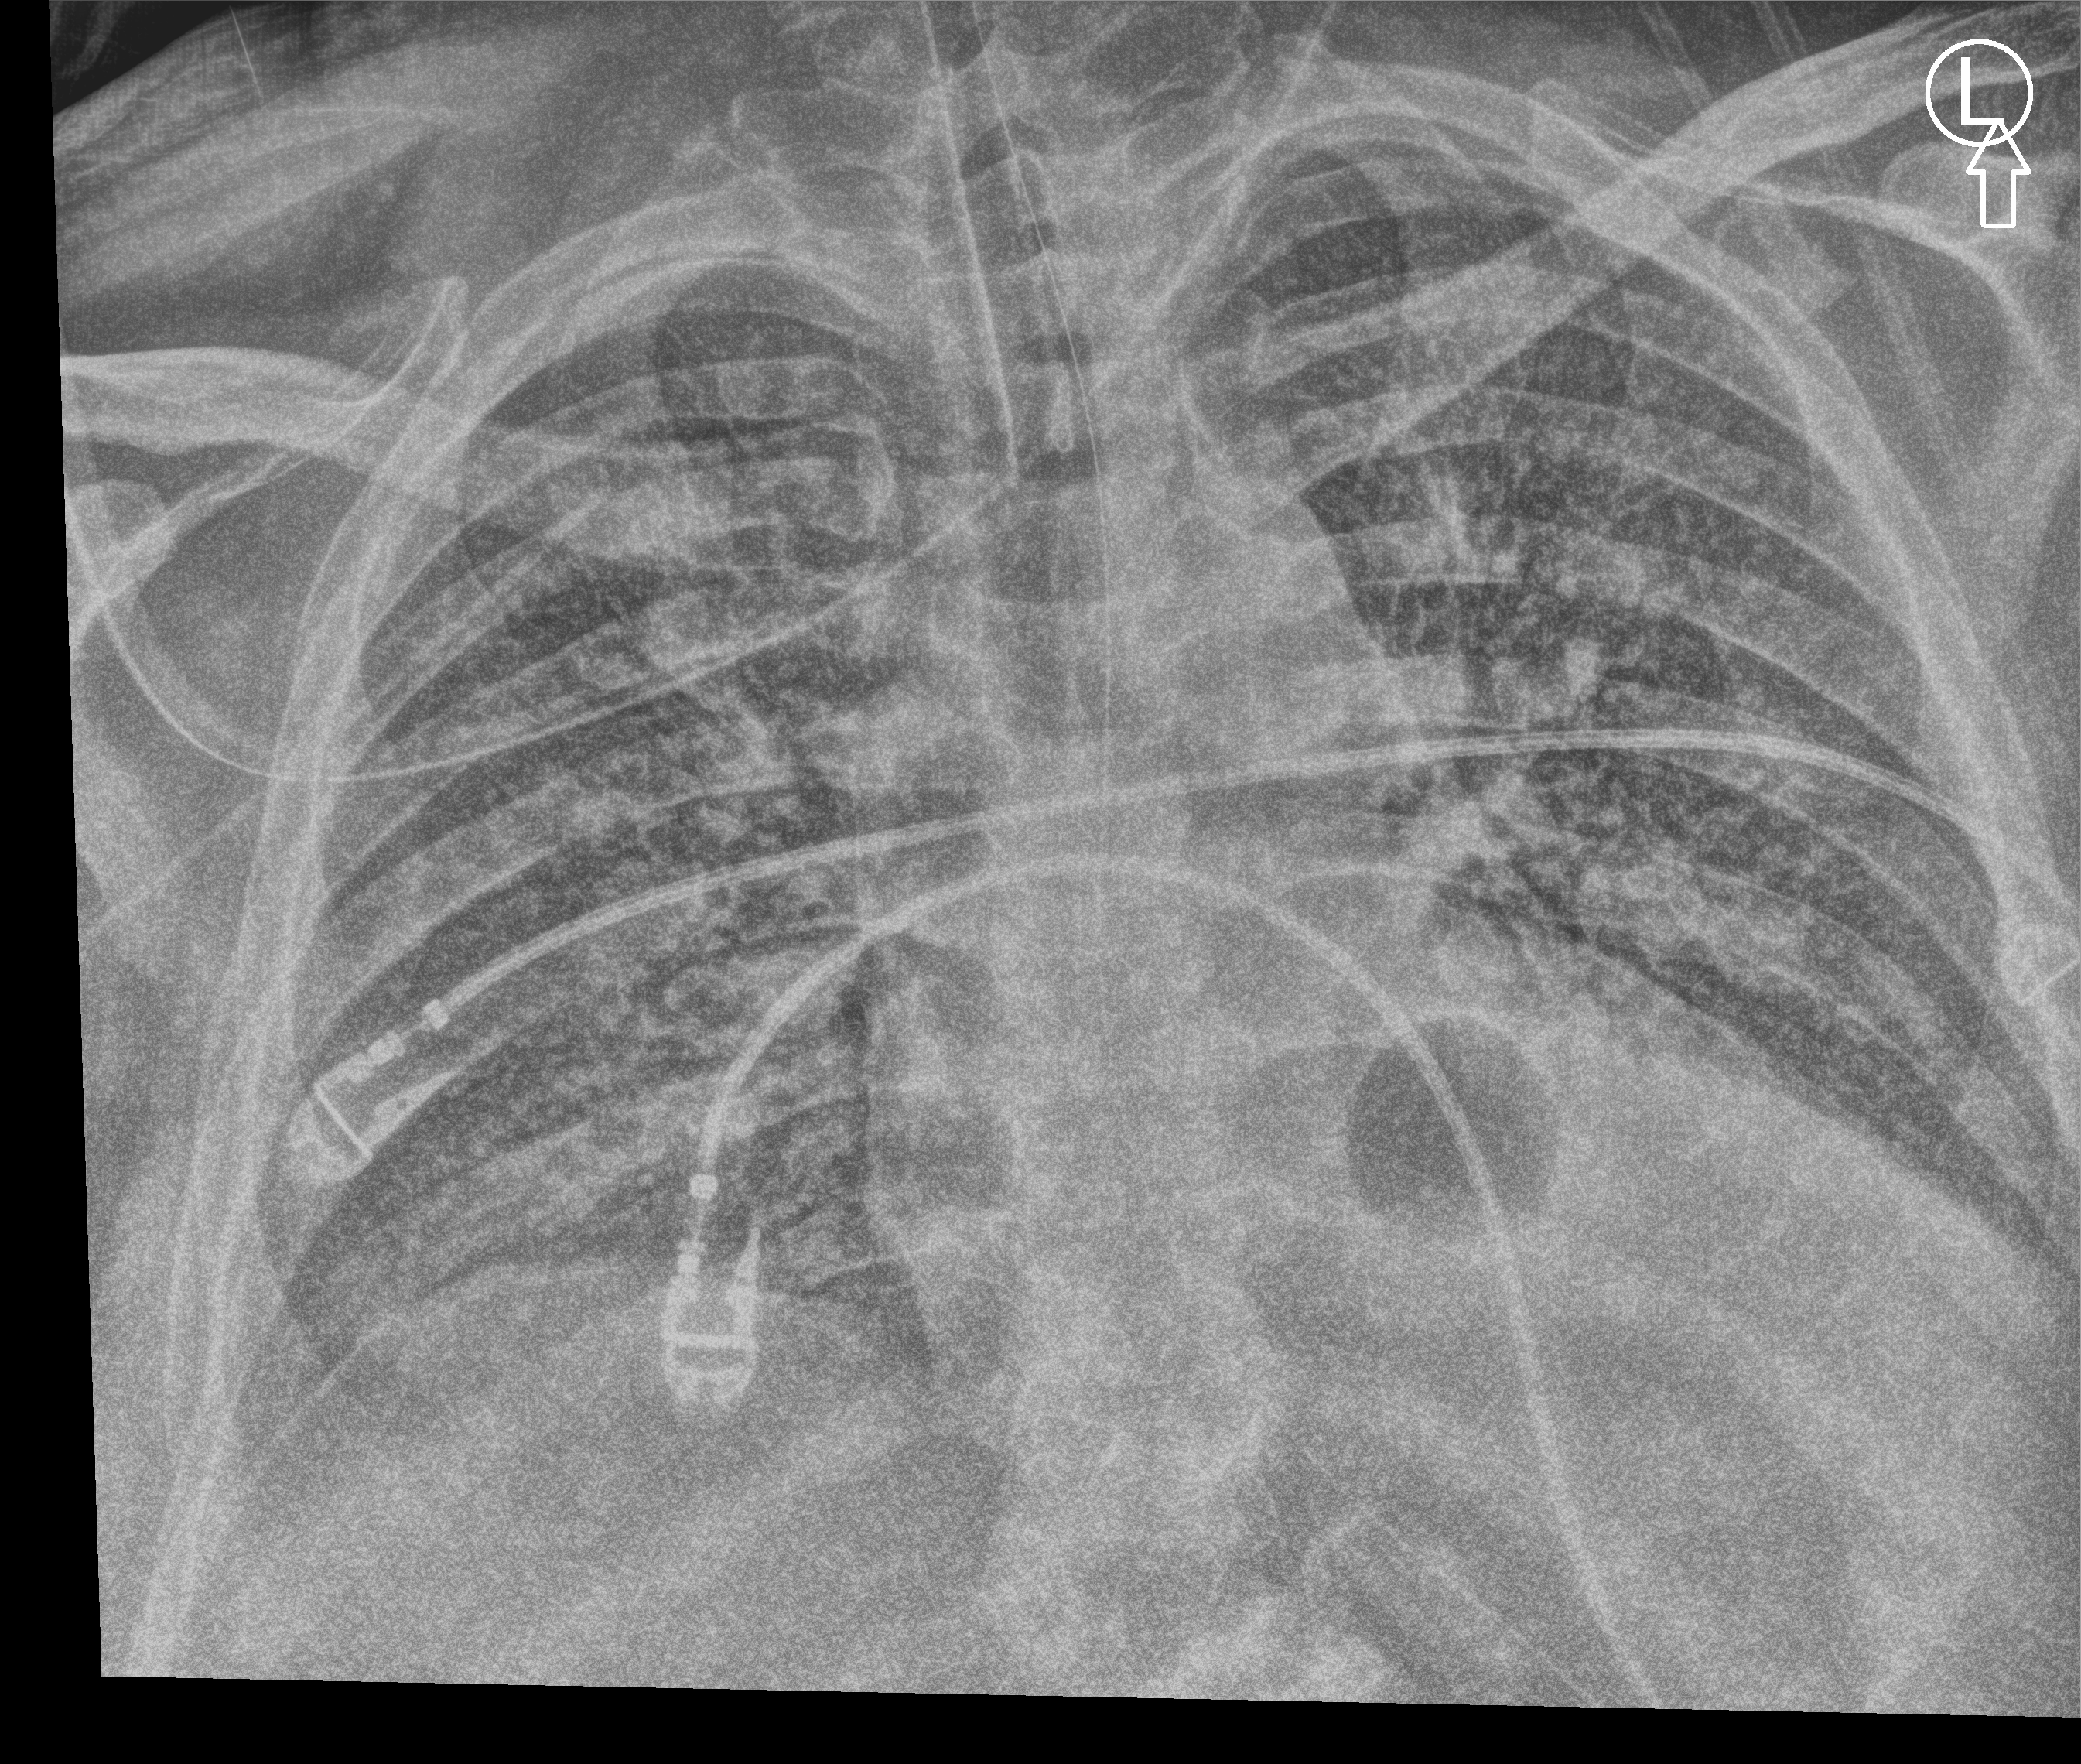
Bedside chest radiograph (computed radiography), anteroposterior (AP) projection. Patient hospitalised with COVID-19, aged 18–59 years.
Admission-level facts for this patient (not findings on this image; timing relative to this image not recorded): length of hospital stay: 26 days; other chronic lung disease (admission record): no; admitted to intensive care during this hospital stay: yes.